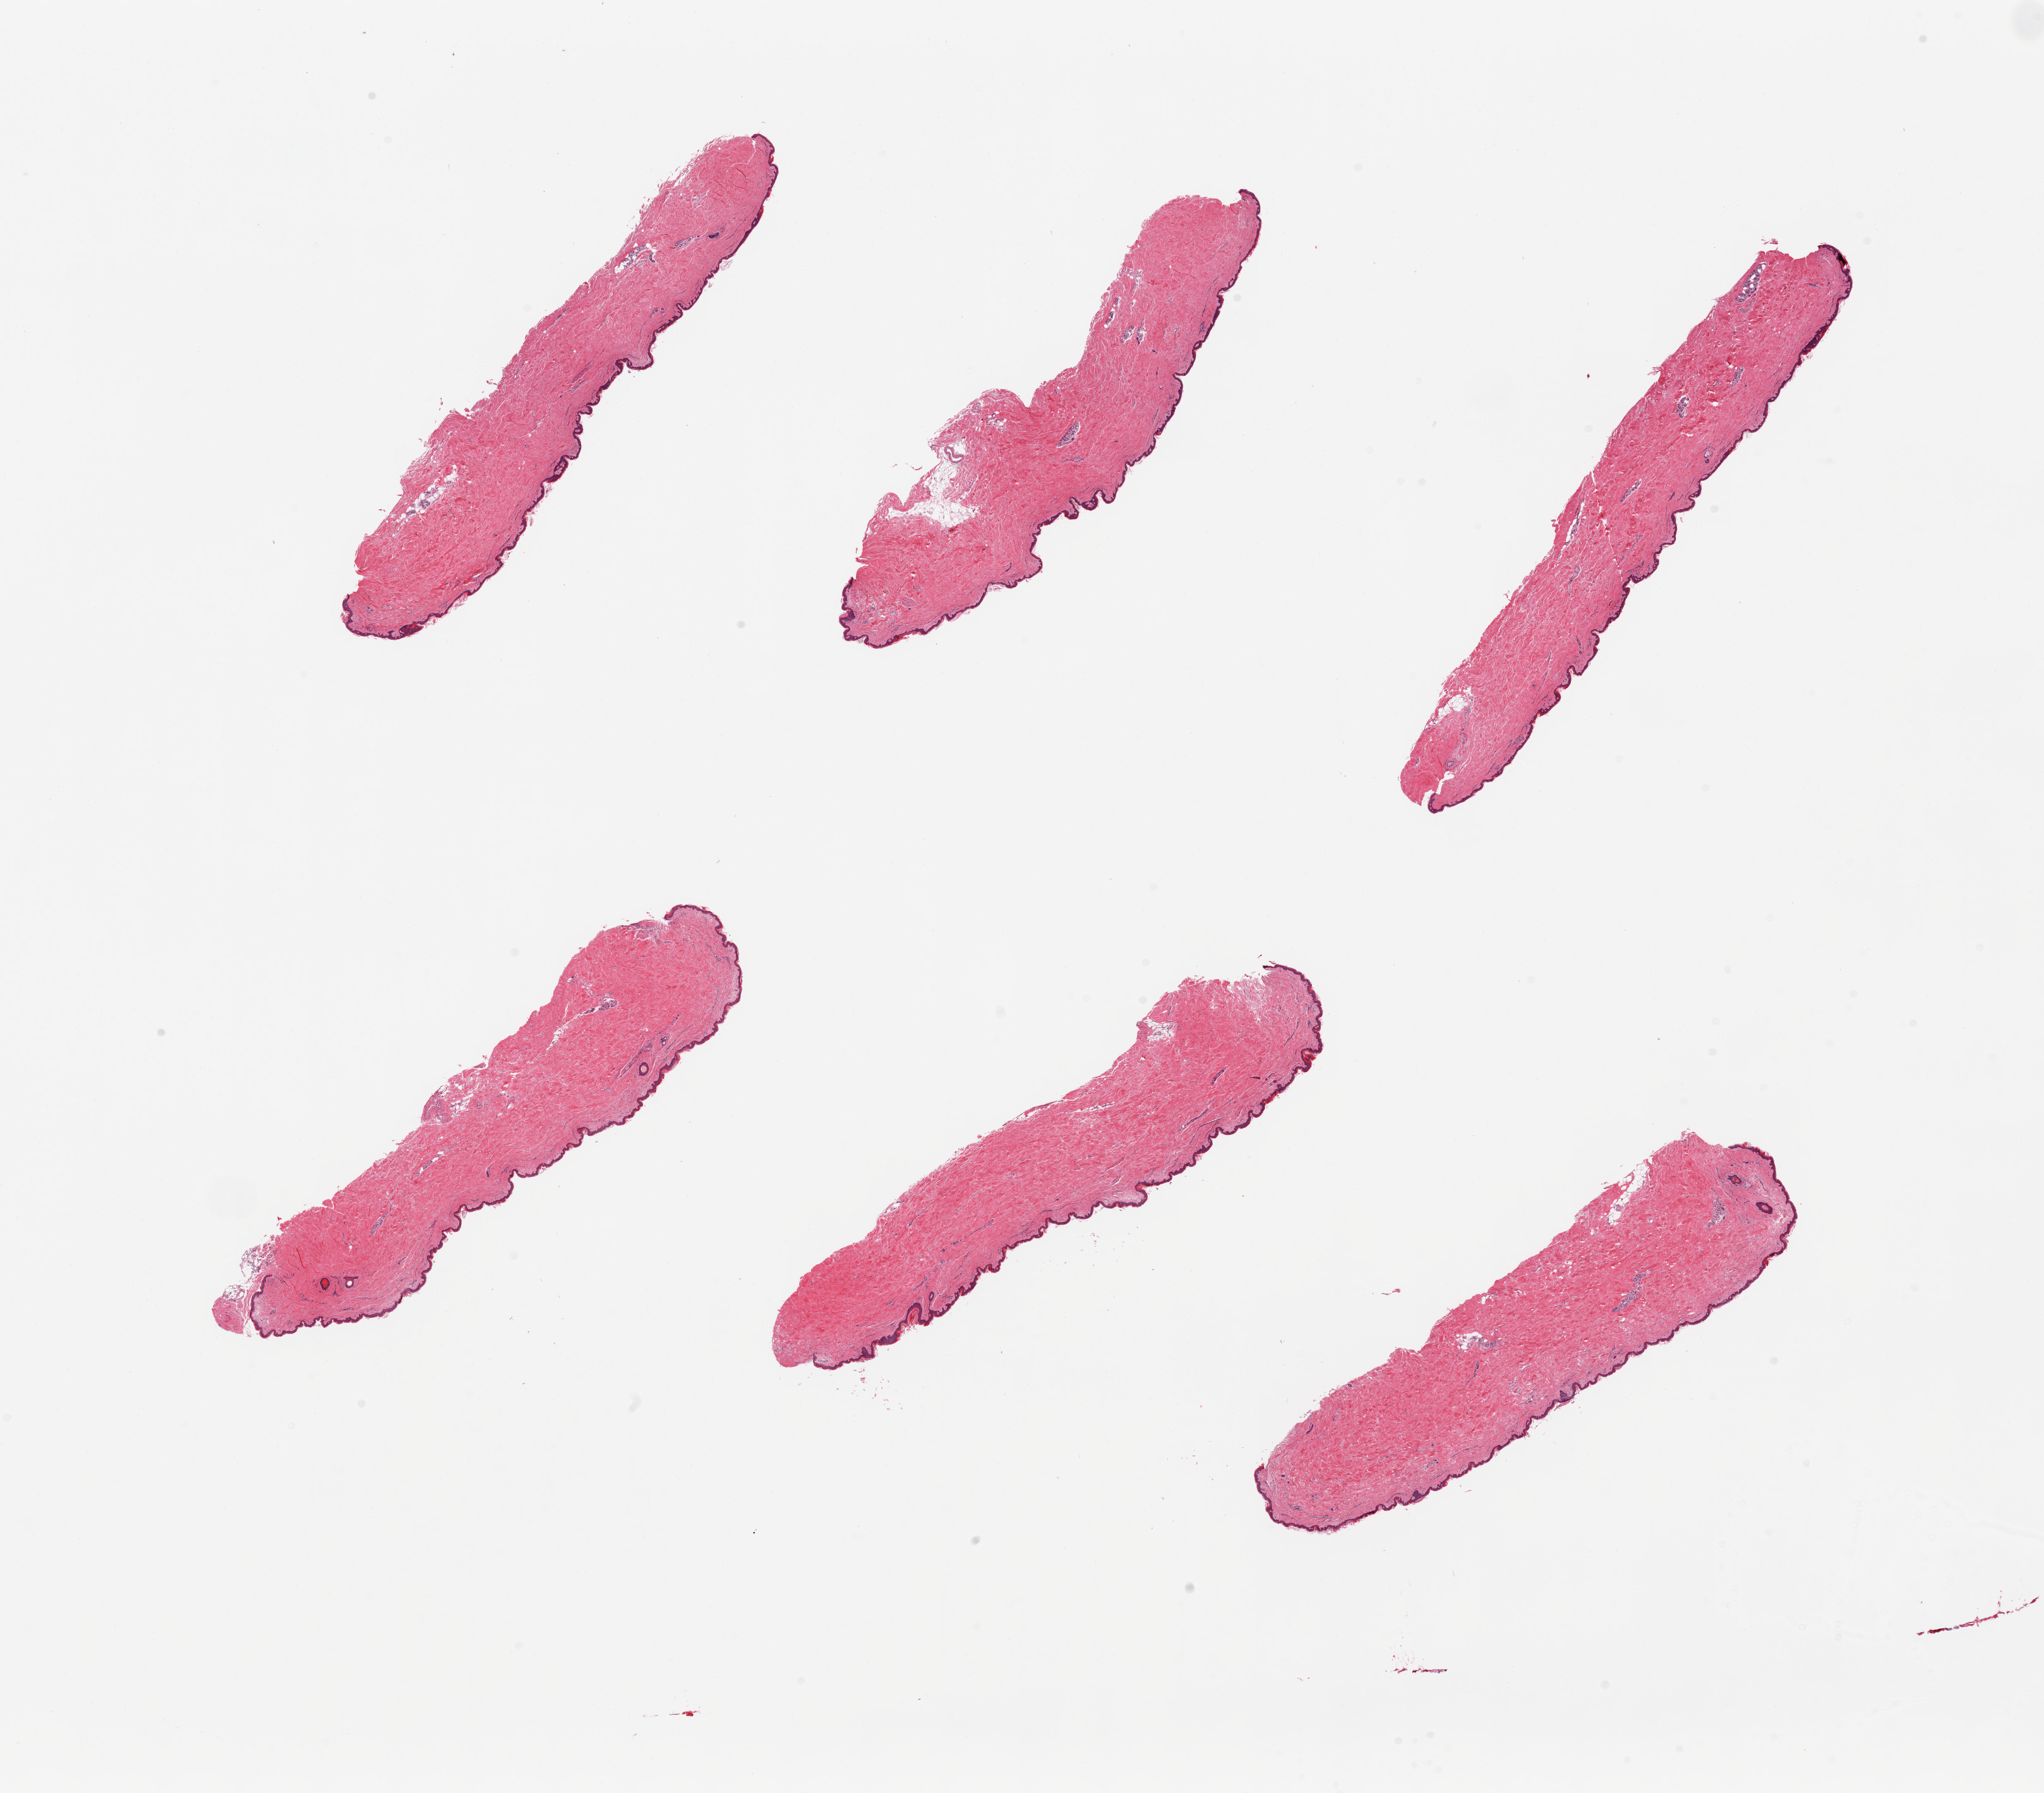
Digitized hematoxylin and eosin (H&E)-stained section — whole scanned area (about 25.6 x 22.4 mm, acquisition: 20x scan) shown as a low-resolution overview, PAXgene-fixed, paraffin-embedded tissue, target tissue: skin of suprapubic region, tissue donor sample.
Reviewer comment on this tissue sample: 6 pieces; attenuated epidermis,(19um); well dissected; <5% dermal fat.